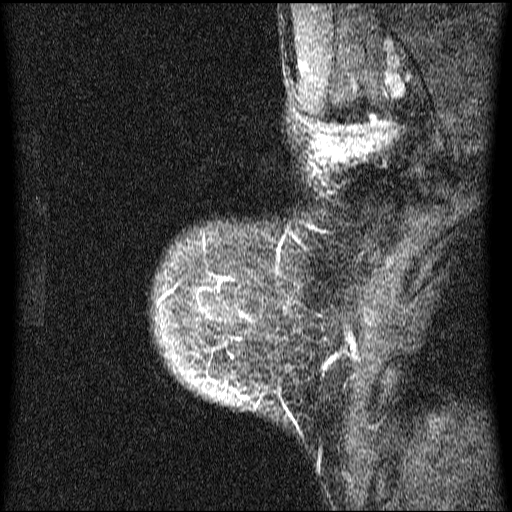
Breast MRI (dynamic contrast-enhanced), one sagittal slice; slice 56 of 64 in the series (ordered by position); dynamic contrast-enhanced series, image 2 of 4 at this slice position (ordered by acquisition); 1.5 T; TE 4.2 ms, TR 9.1 ms; 2 mm slice thickness; 512 × 512 image matrix, field of view 180 × 180 mm. Patient: female, 33 years.
Annotated regions visible in this slice (semi-automatic segmentation, software-assisted and operator-edited):
- analysis volume of interest (the breast-tissue region the enhancement analysis was run in; not a lesion): bounding box [x1, y1, x2, y2] px = [156, 151, 336, 422]
- tumour enhancement mask (voxels above the 70 % enhancement threshold inside the analysis volume of interest): [158, 248, 248, 400]